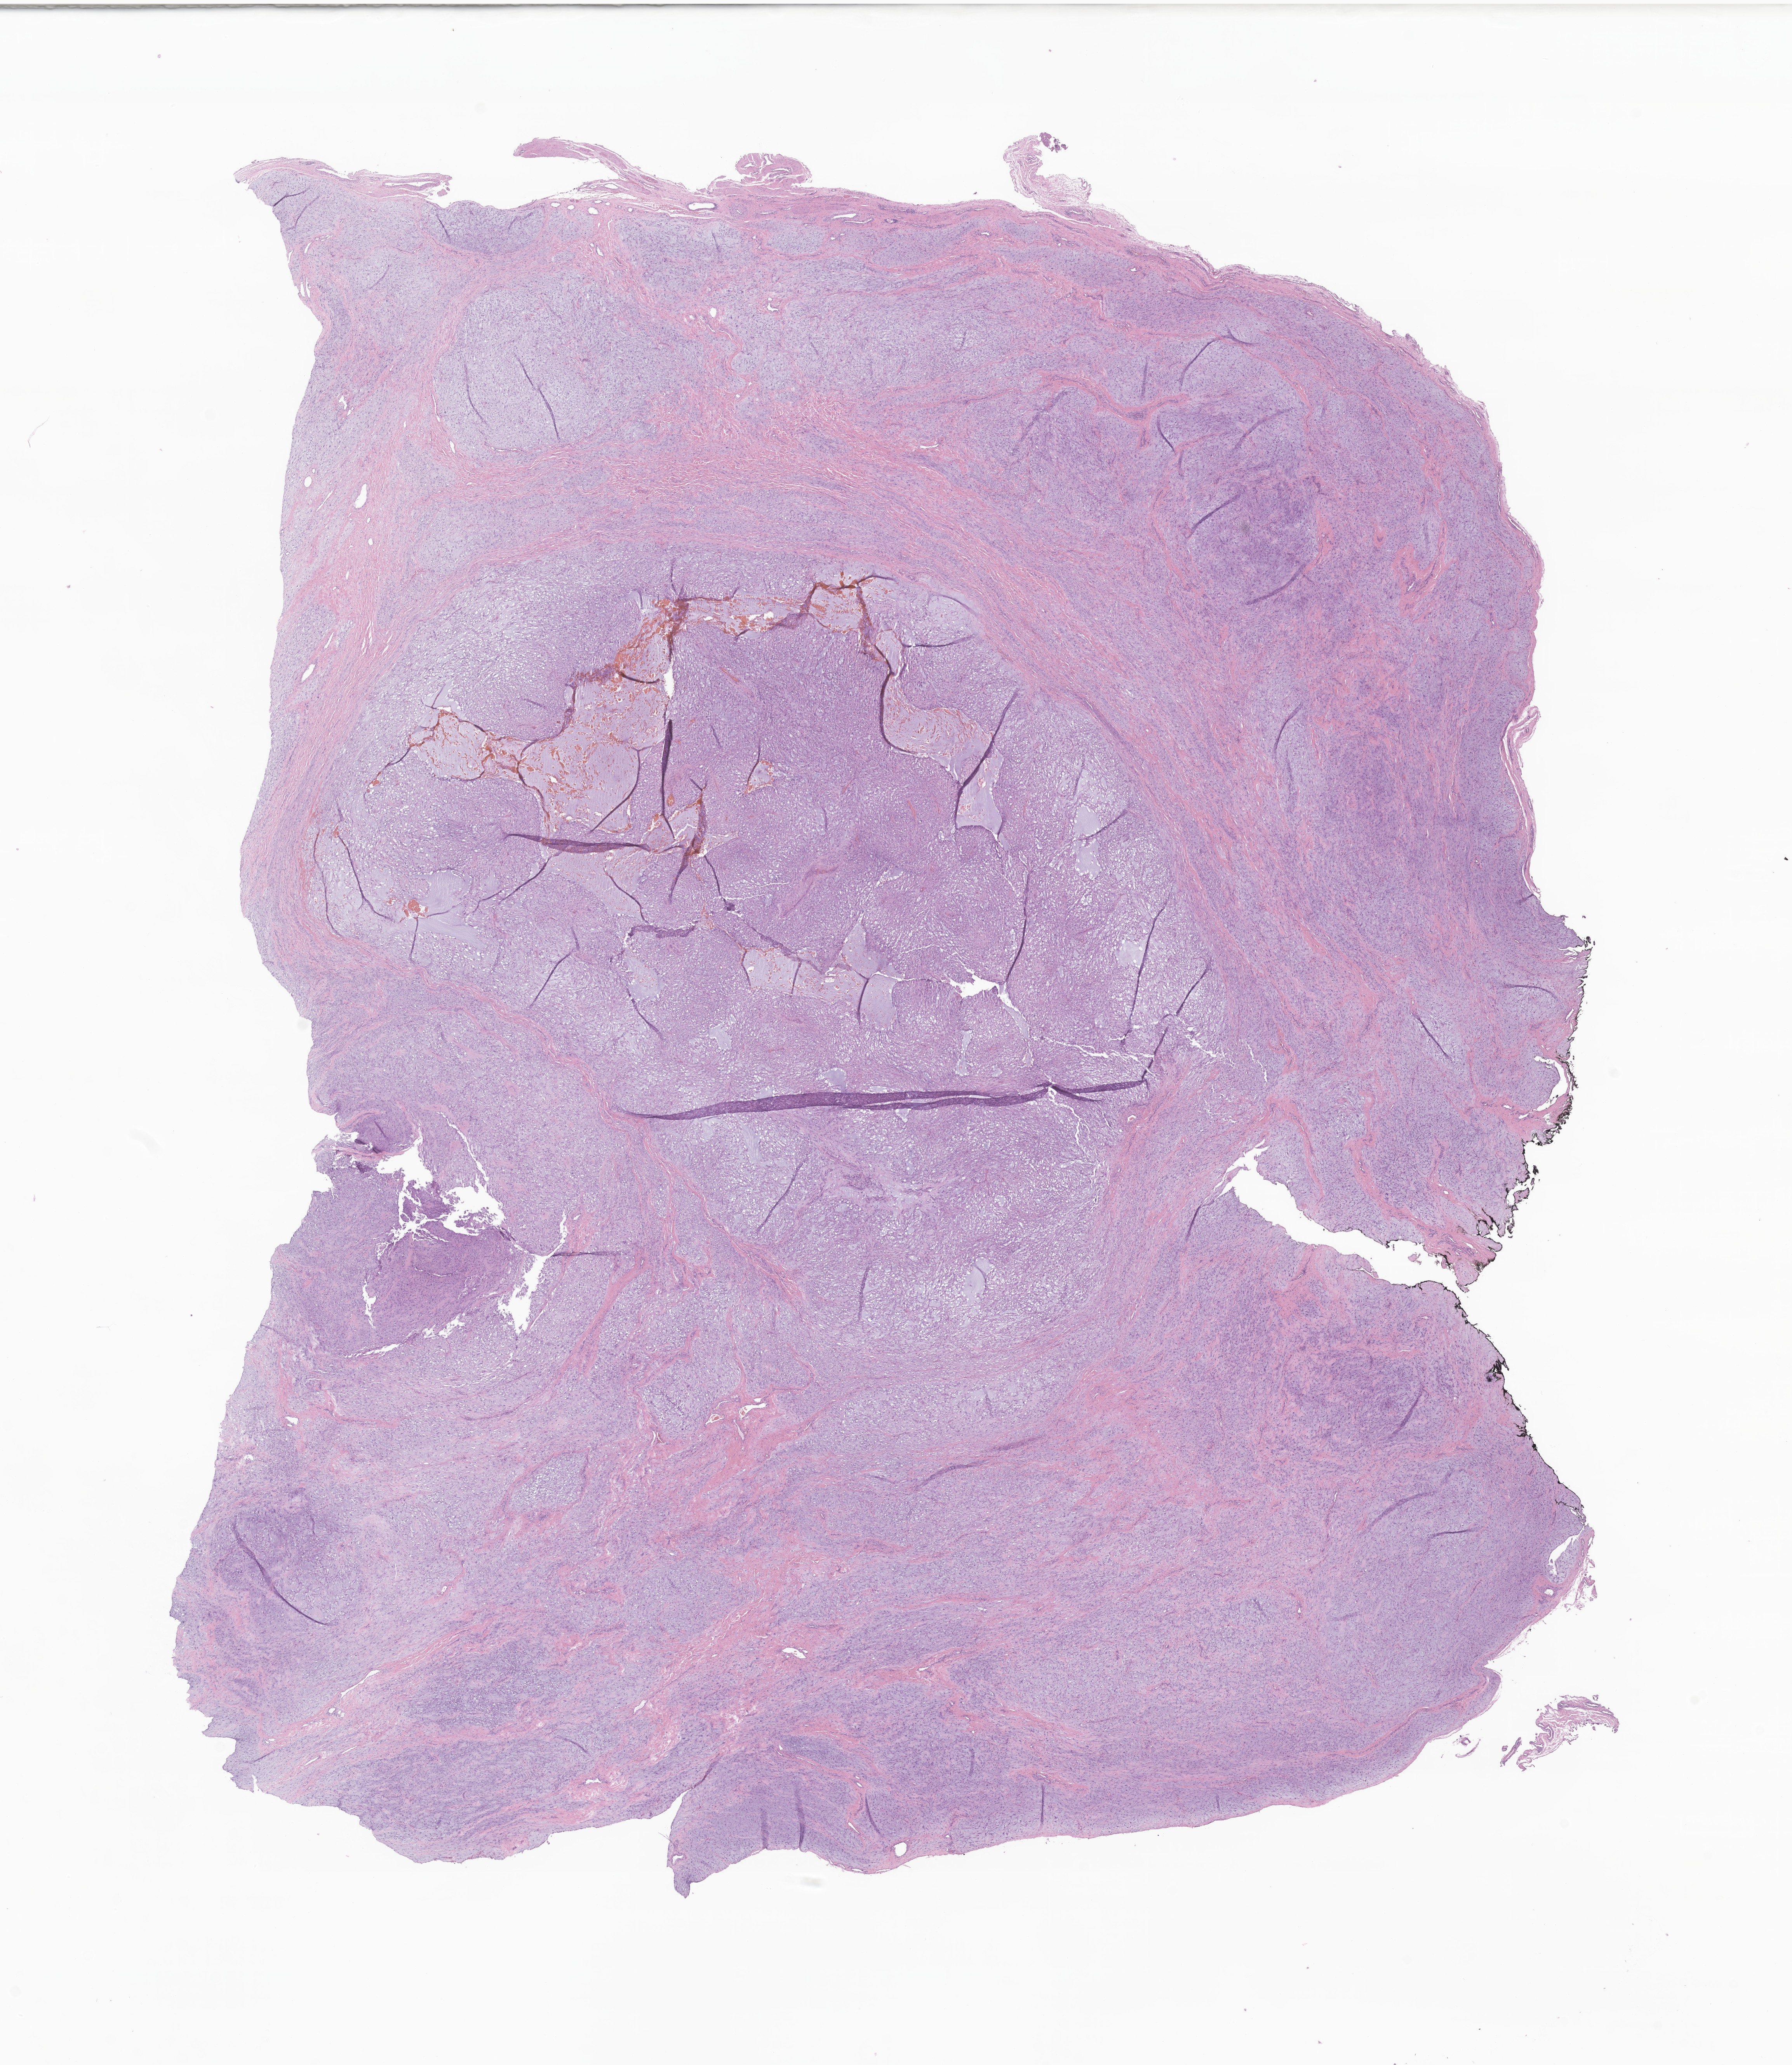
H&E whole-slide image of tumor tissue from the vagina — whole scanned area (about 19.4 x 22.4 mm) shown as a low-resolution overview. FFPE section. Patient: female, age 193 months (16 years 1 month).
Recorded diagnosis: Spindle cell carcinoma, NOS.